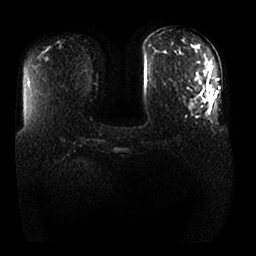
Breast MRI, one axial slice; position 8 of 25 along the scan axis; diffusion-weighted series; image 2 of 4 stored at this slice position (different b-values; order by instance number); 1.5 T; 256 × 256 image matrix. Female patient.
Structures marked on this image (expert manual segmentation):
- tumour on diffusion-weighted imaging: bounding box (x1, y1, x2, y2) in pixels: (206, 98, 209, 102)